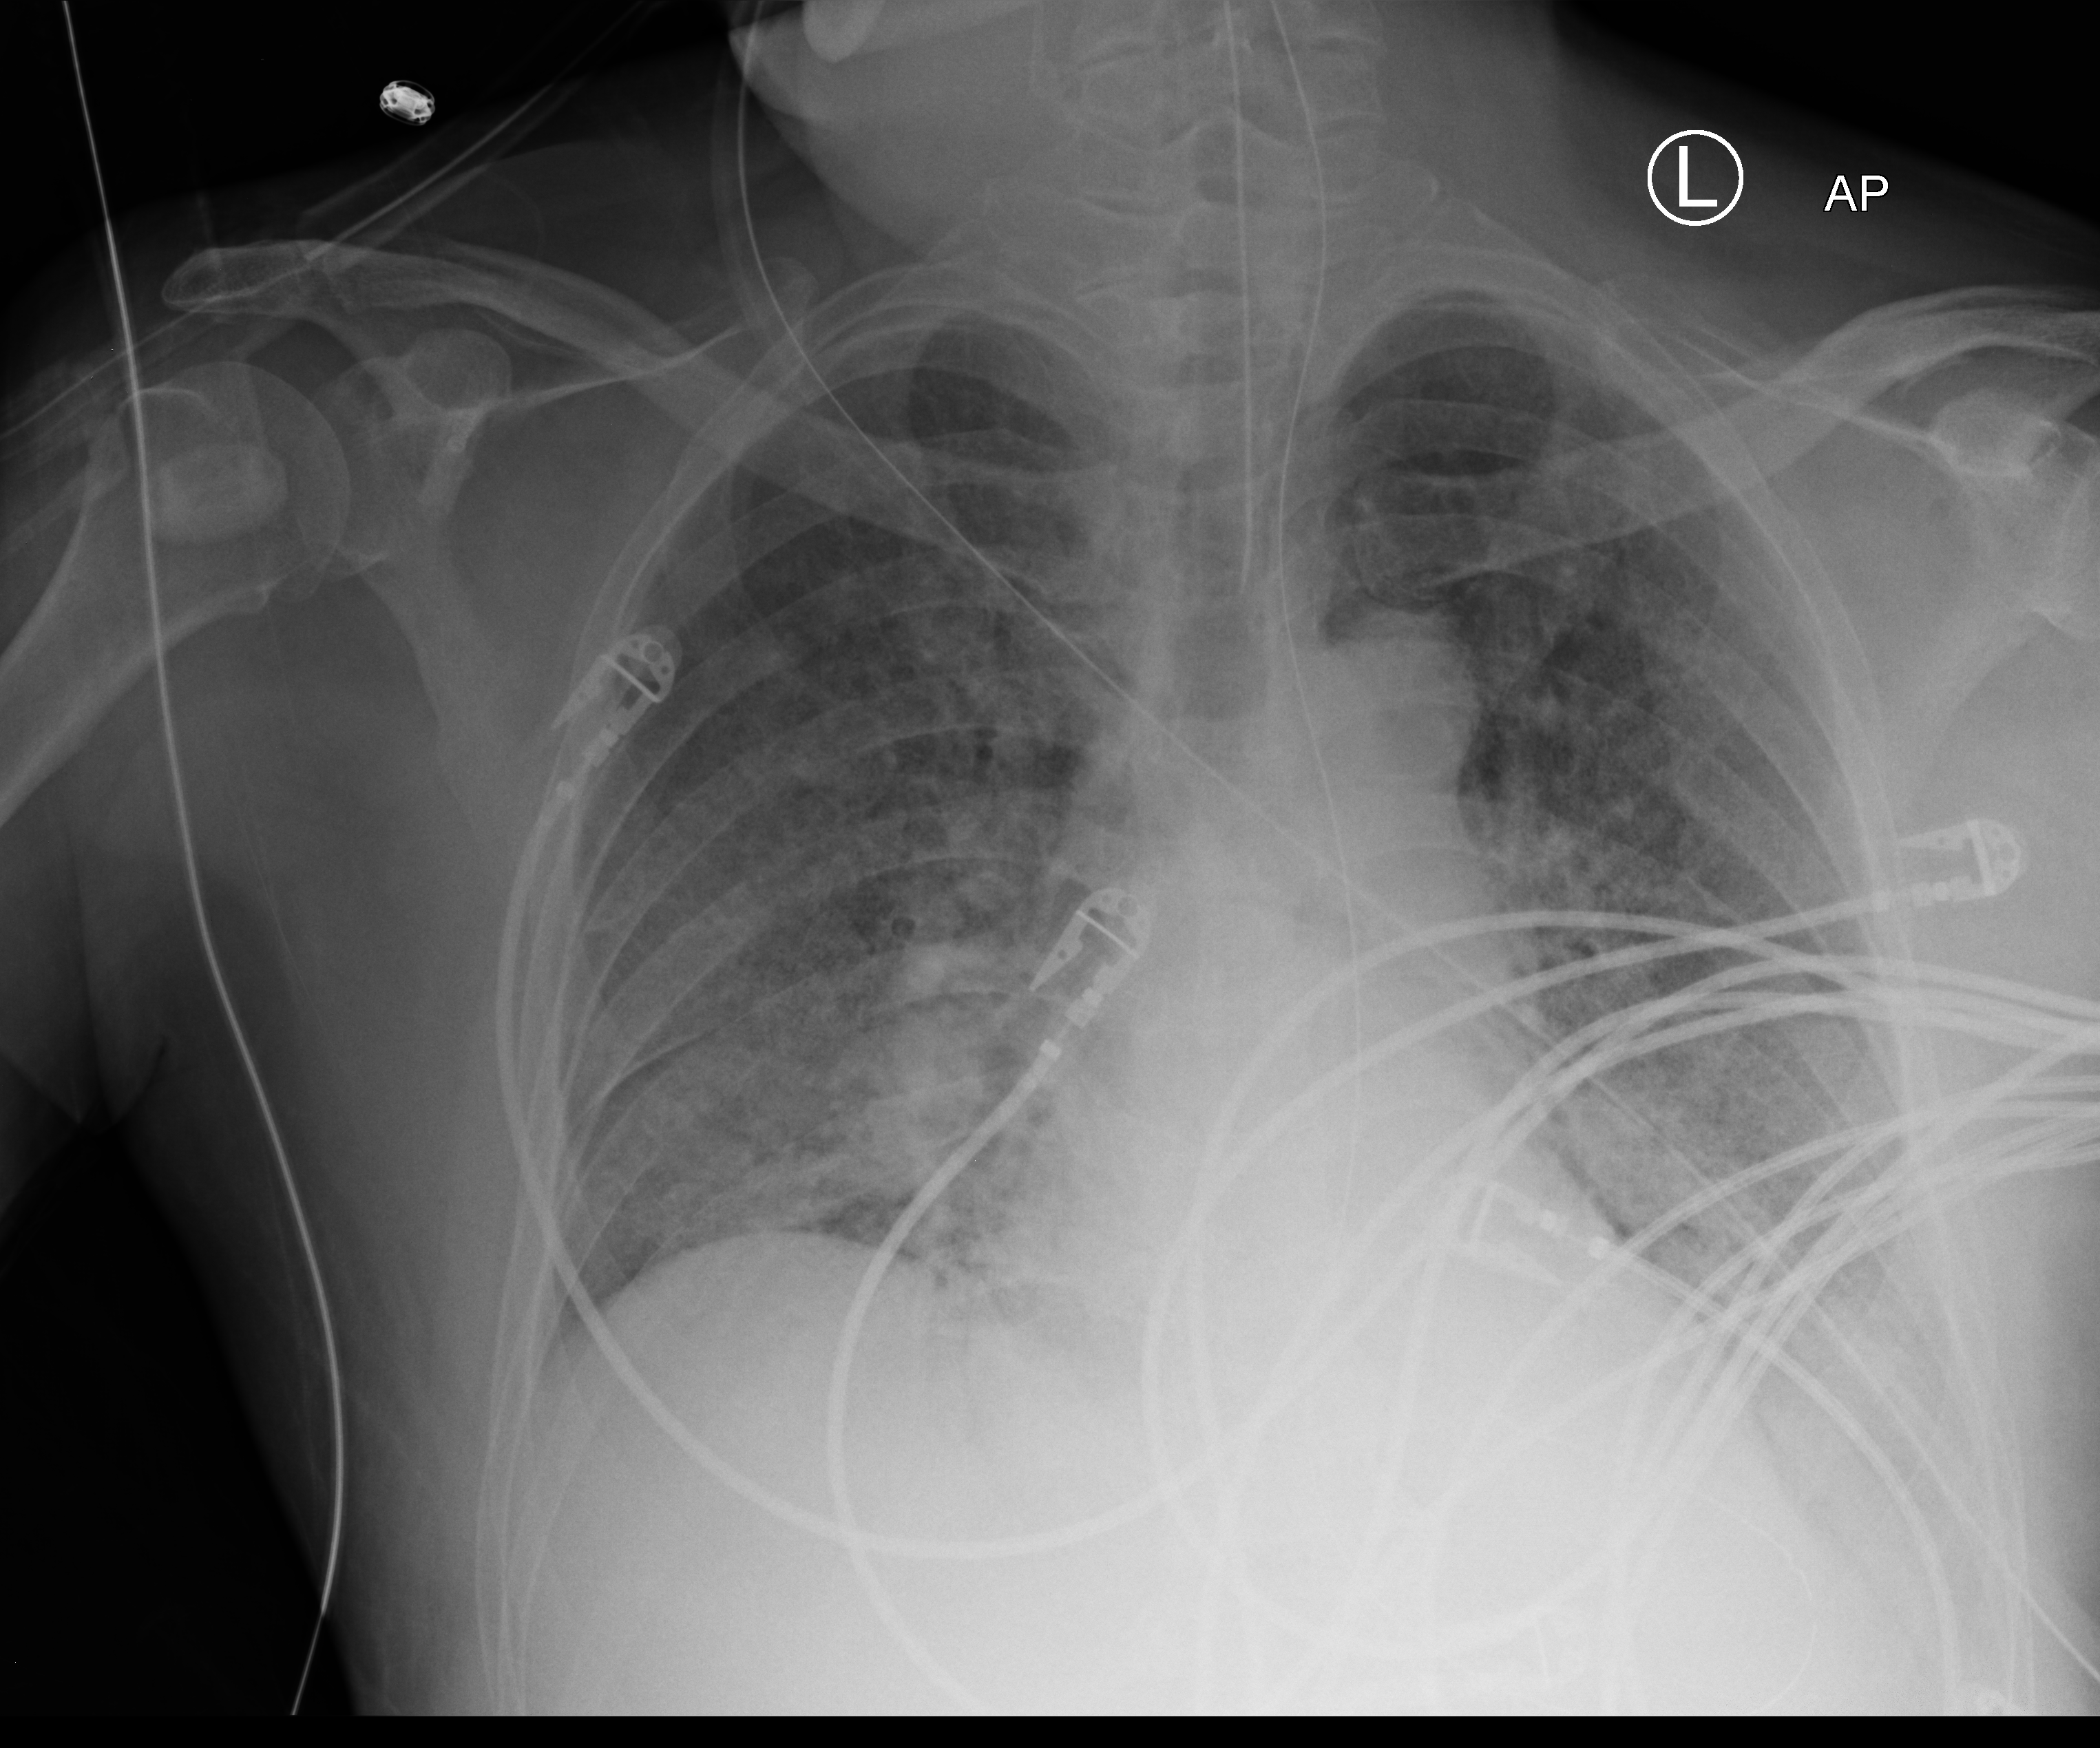
Portable chest radiograph, anteroposterior (AP) projection. Male patient hospitalised with COVID-19, age 60–74 years.
Hospital-stay facts (about this admission, not read from this image; timing relative to this image not recorded):
- smoking status (admission record): former